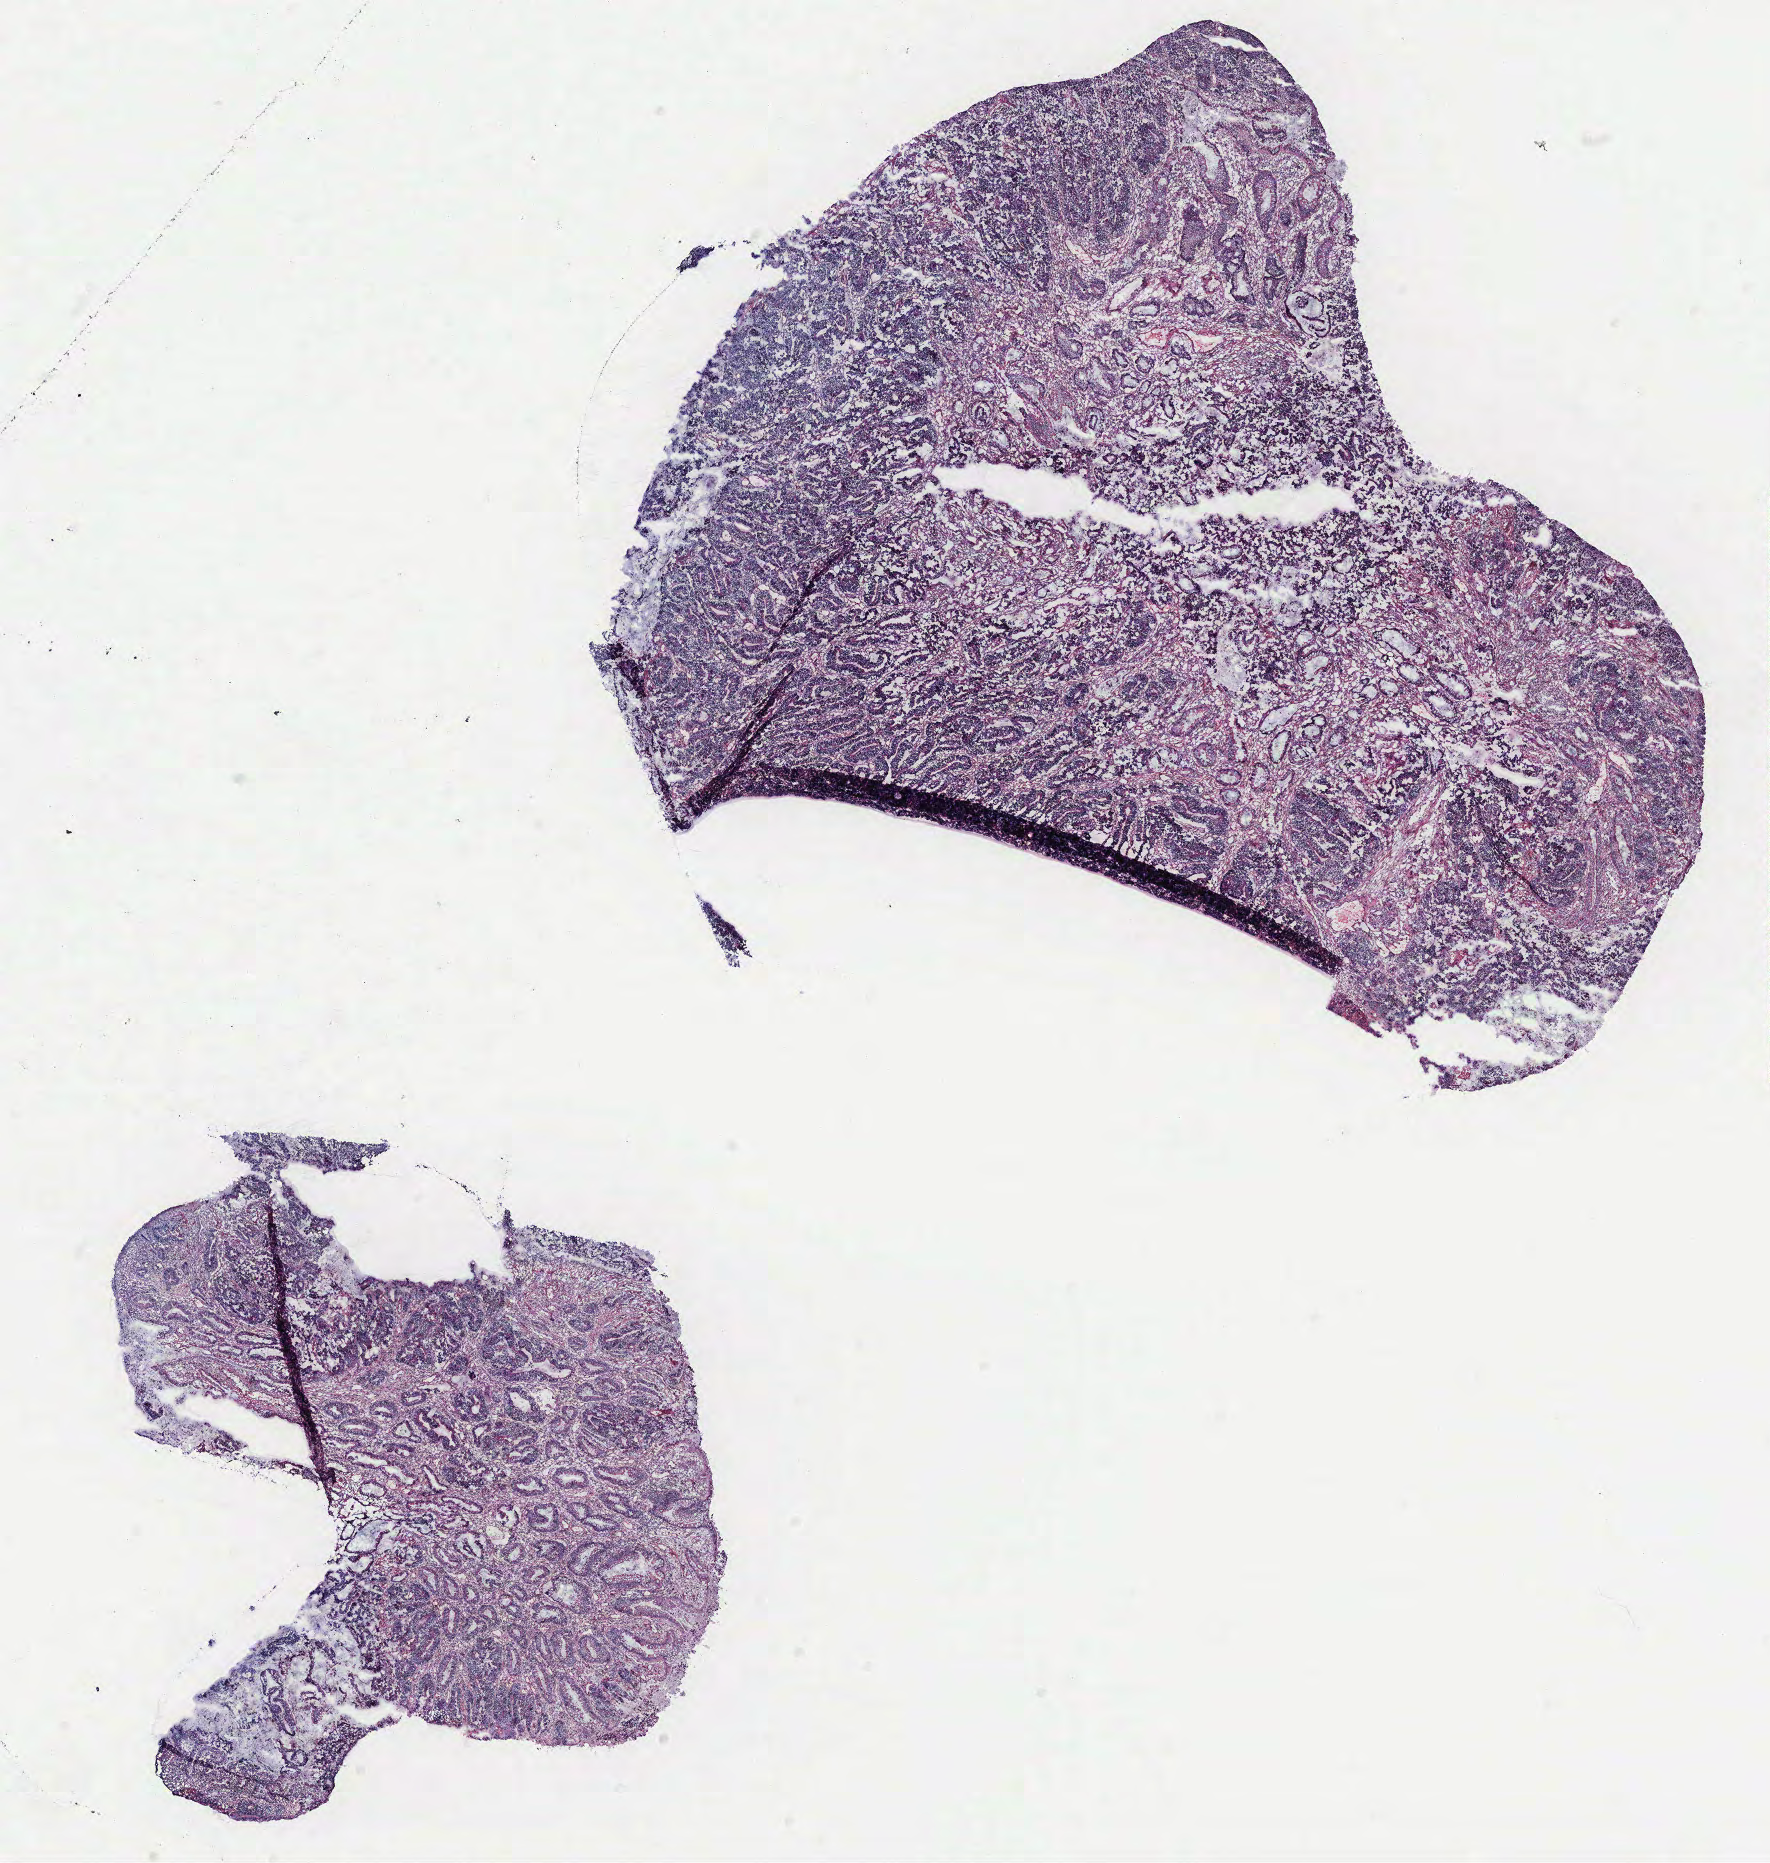
Whole-slide histology image, H&E, low-resolution overview of the scanned area, about 14.2 x 14.9 mm; colon, tissue type not recorded. Patient sex: female.
• patient diagnosis: Adenocarcinoma, NOS